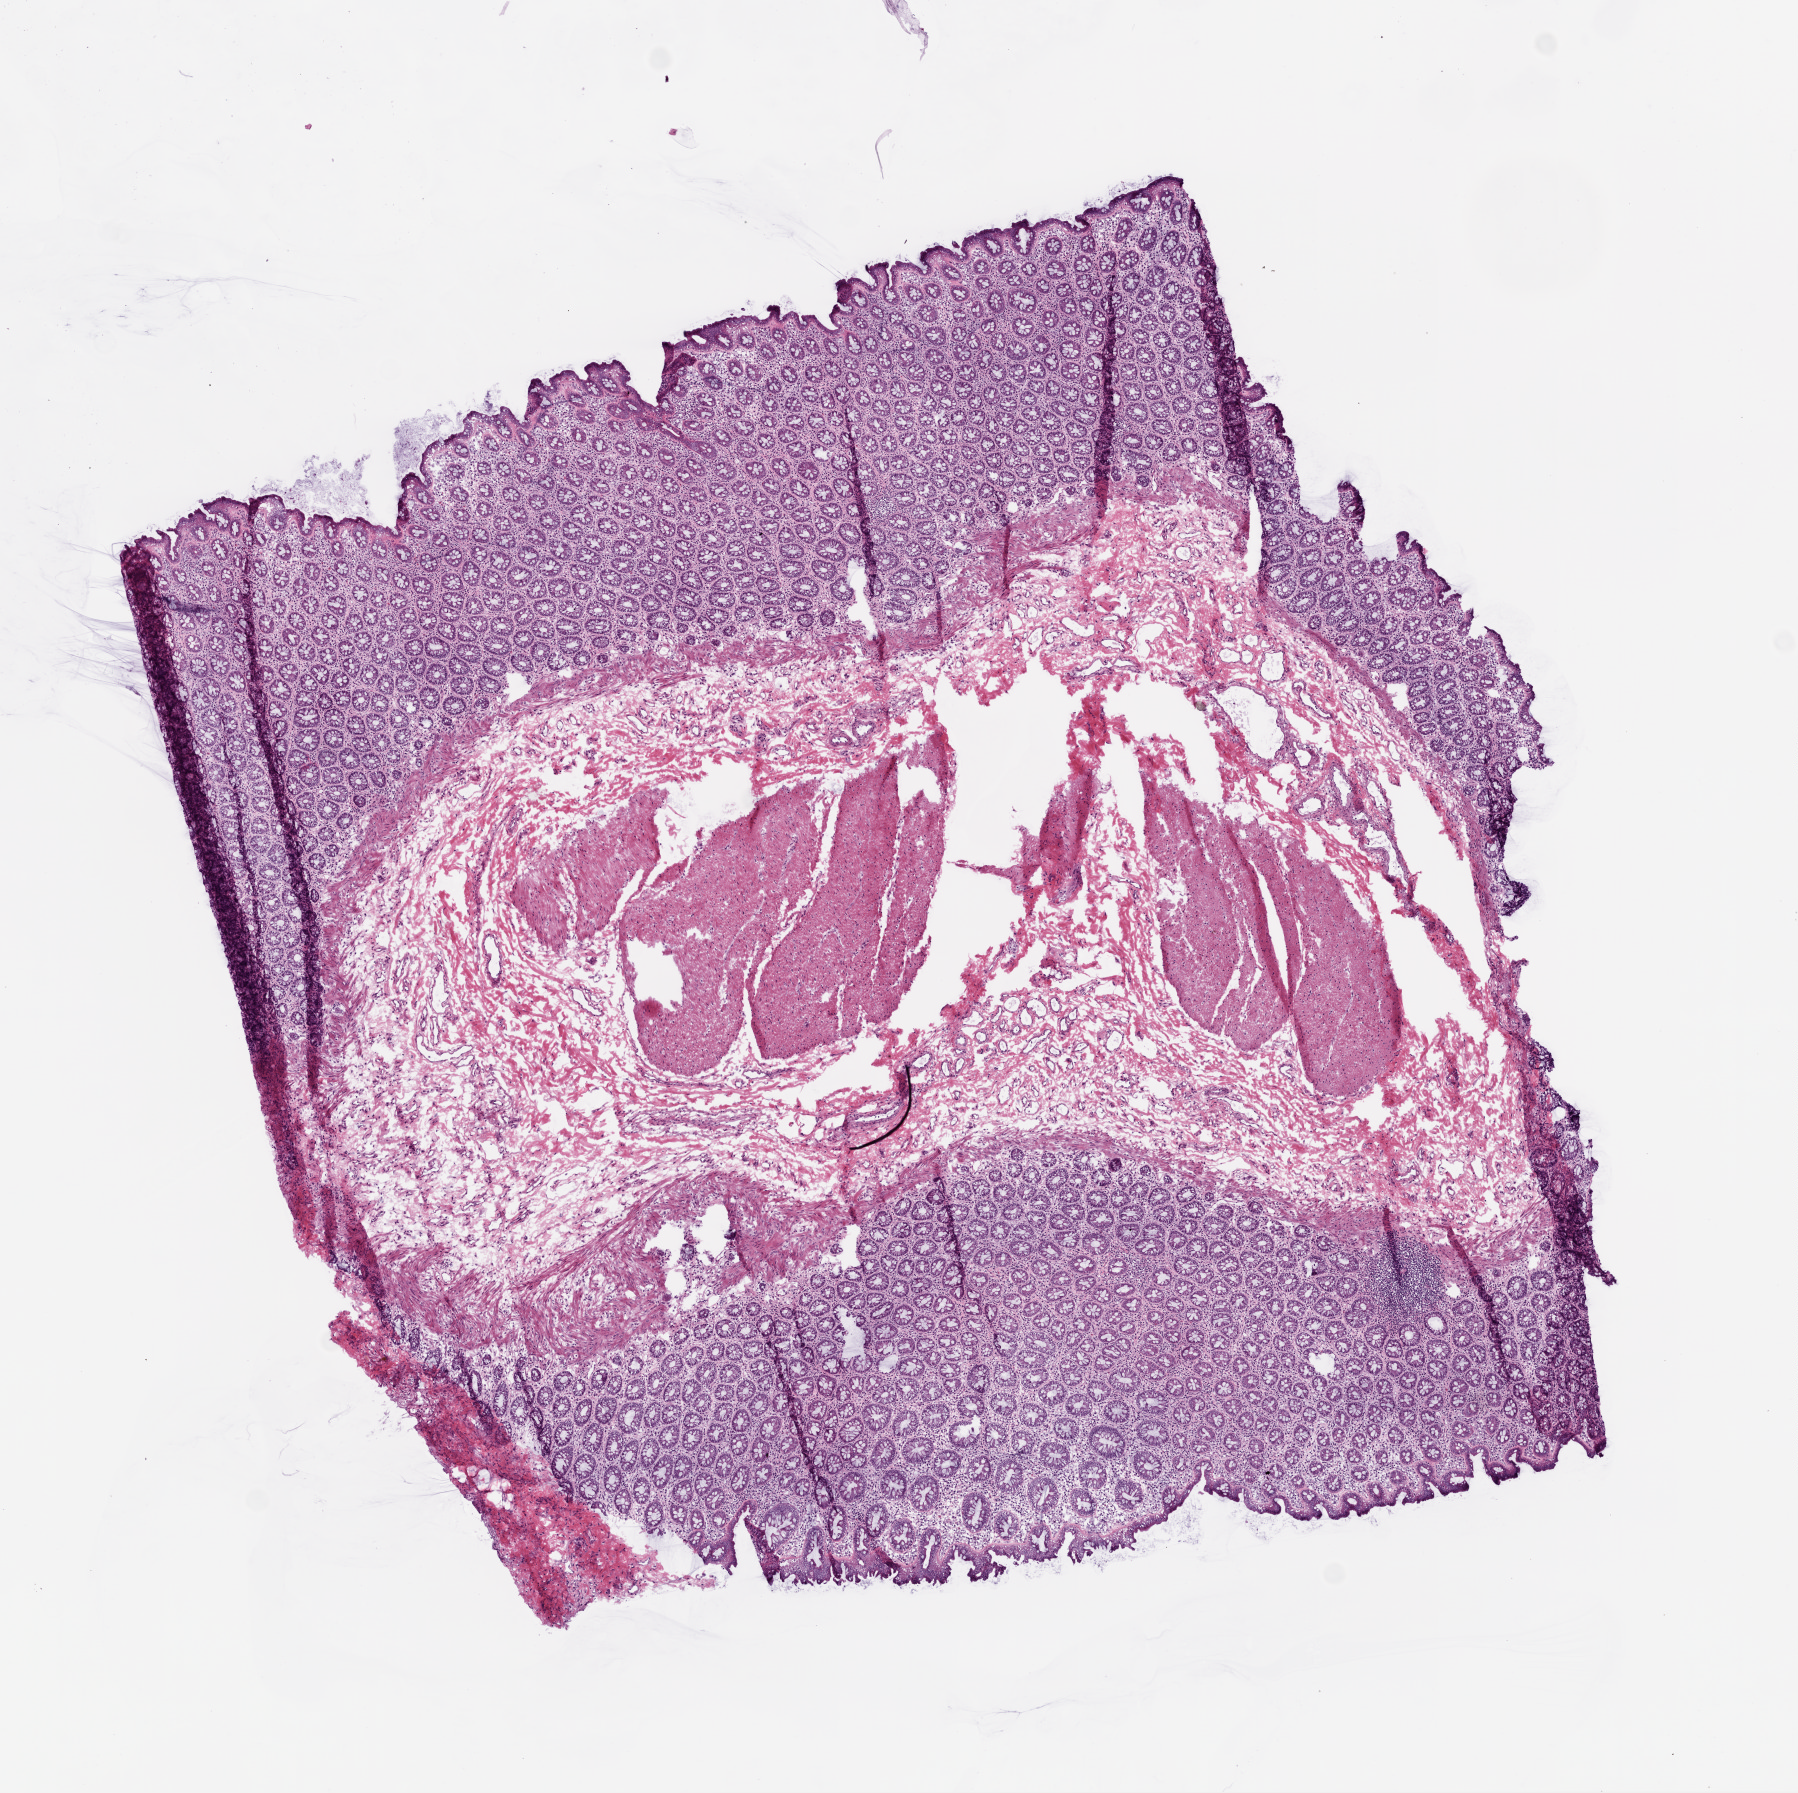
H&E whole-slide image, low-resolution overview of the scanned area, about 7.3 x 7.2 mm; frozen section; colon, solid tissue normal (non-tumour tissue) sample. Patient: male, age at initial diagnosis 78 years.
This section: solid tissue normal sample (biorepository sample class). Patient diagnosis: Adenocarcinoma, NOS (sigmoid colon).